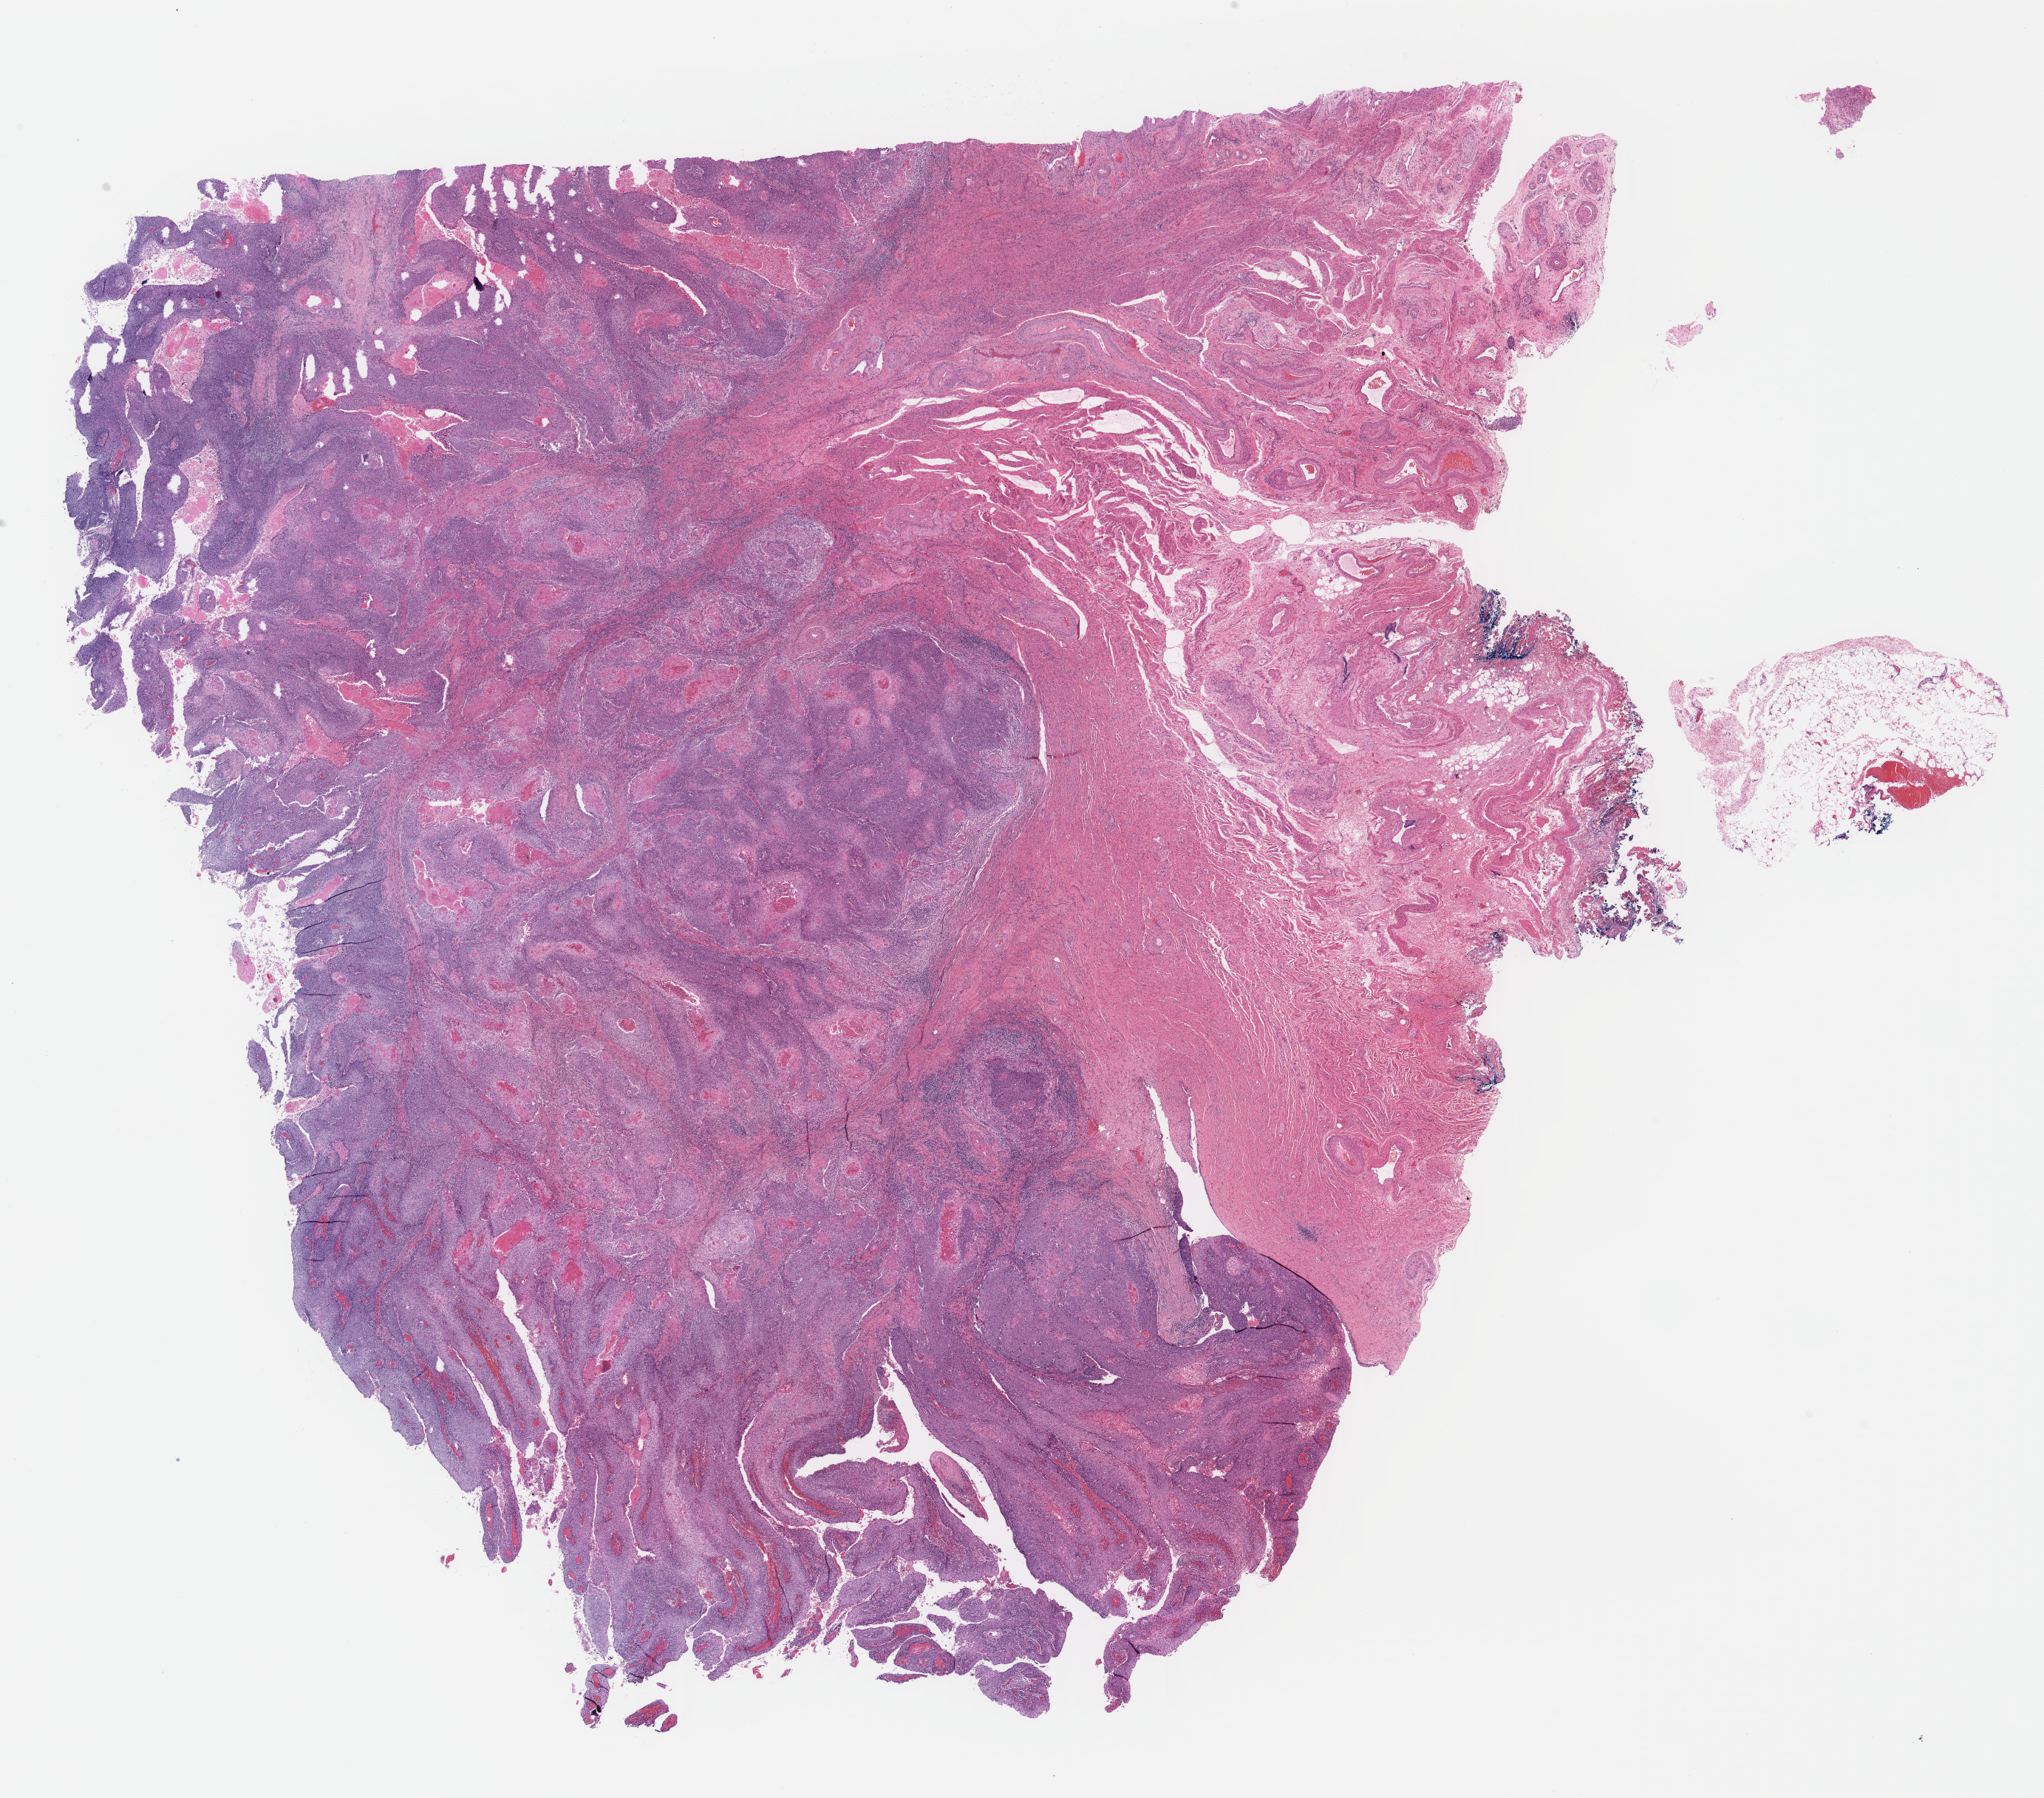
H&E whole-slide image, whole scanned area (about 21.7 x 19.1 mm) shown as a low-resolution overview, FFPE section, cervix, primary tumour sample. Female, age 68 years at initial diagnosis. Histologic grade: G1 (well differentiated).
* diagnosis: Squamous cell carcinoma, keratinizing, NOS (cervix uteri)
* FIGO stage: IIA2